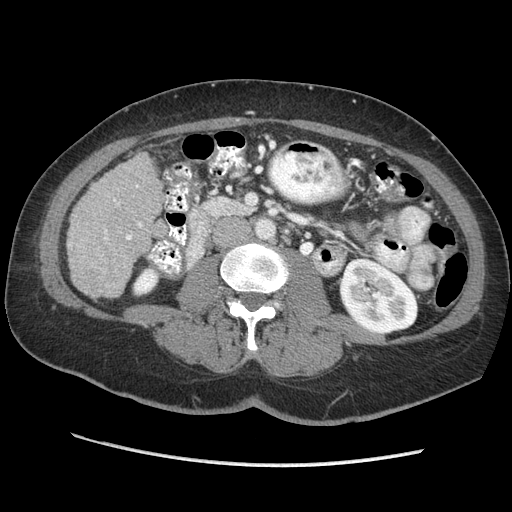
Contrast-enhanced abdominal CT (liver protocol), one axial slice. Slice 97 of 170 in the series (ordered by position). Reconstruction kernel STANDARD. 140 kVp. Soft-tissue window (W 400 / L 40 HU). 2.5 mm slice thickness. 512 × 512 image matrix, field of view 360 × 360 mm. From the clinical record (not read from this slice): diagnosis: hepatocellular carcinoma (patient treated with transarterial chemoembolisation; whether this scan precedes or follows treatment is not stated here); TNM stage (as recorded): Stage-II.
Outlined on this slice (semi-automatic segmentation, software-assisted and operator-edited):
- liver parenchyma outside the tumour (the mass and vessels are separate outlines, so this box may not span the whole liver): bounding box [x1, y1, x2, y2] px = [66, 152, 164, 298]
- liver vessels: [69, 199, 142, 246]